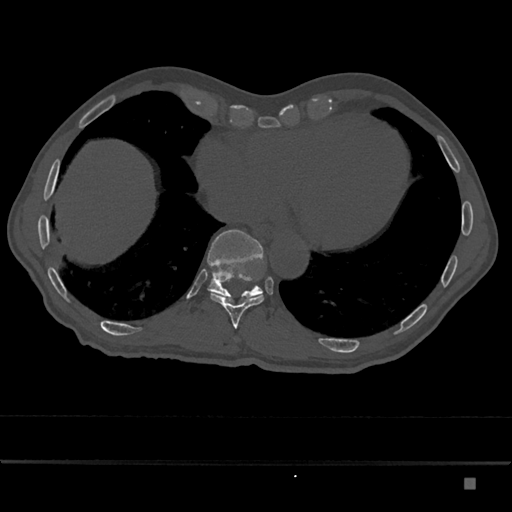
CT including the spine, one axial slice. Reconstruction kernel Br40s/3. 120 kVp. Bone window (W 1800 / L 400 HU). 0.5 mm slice thickness. 512 × 512 image matrix. Male patient, age 72 years. From the clinical record (not read from this slice): primary cancer: prostate.
Outlined on this slice (semi-automatically segmented with operator editing):
- T10 vertebra: box from (x=210, y=293) to (x=264, y=329) px
- T11 vertebra: (x=207, y=230)–(x=263, y=302)